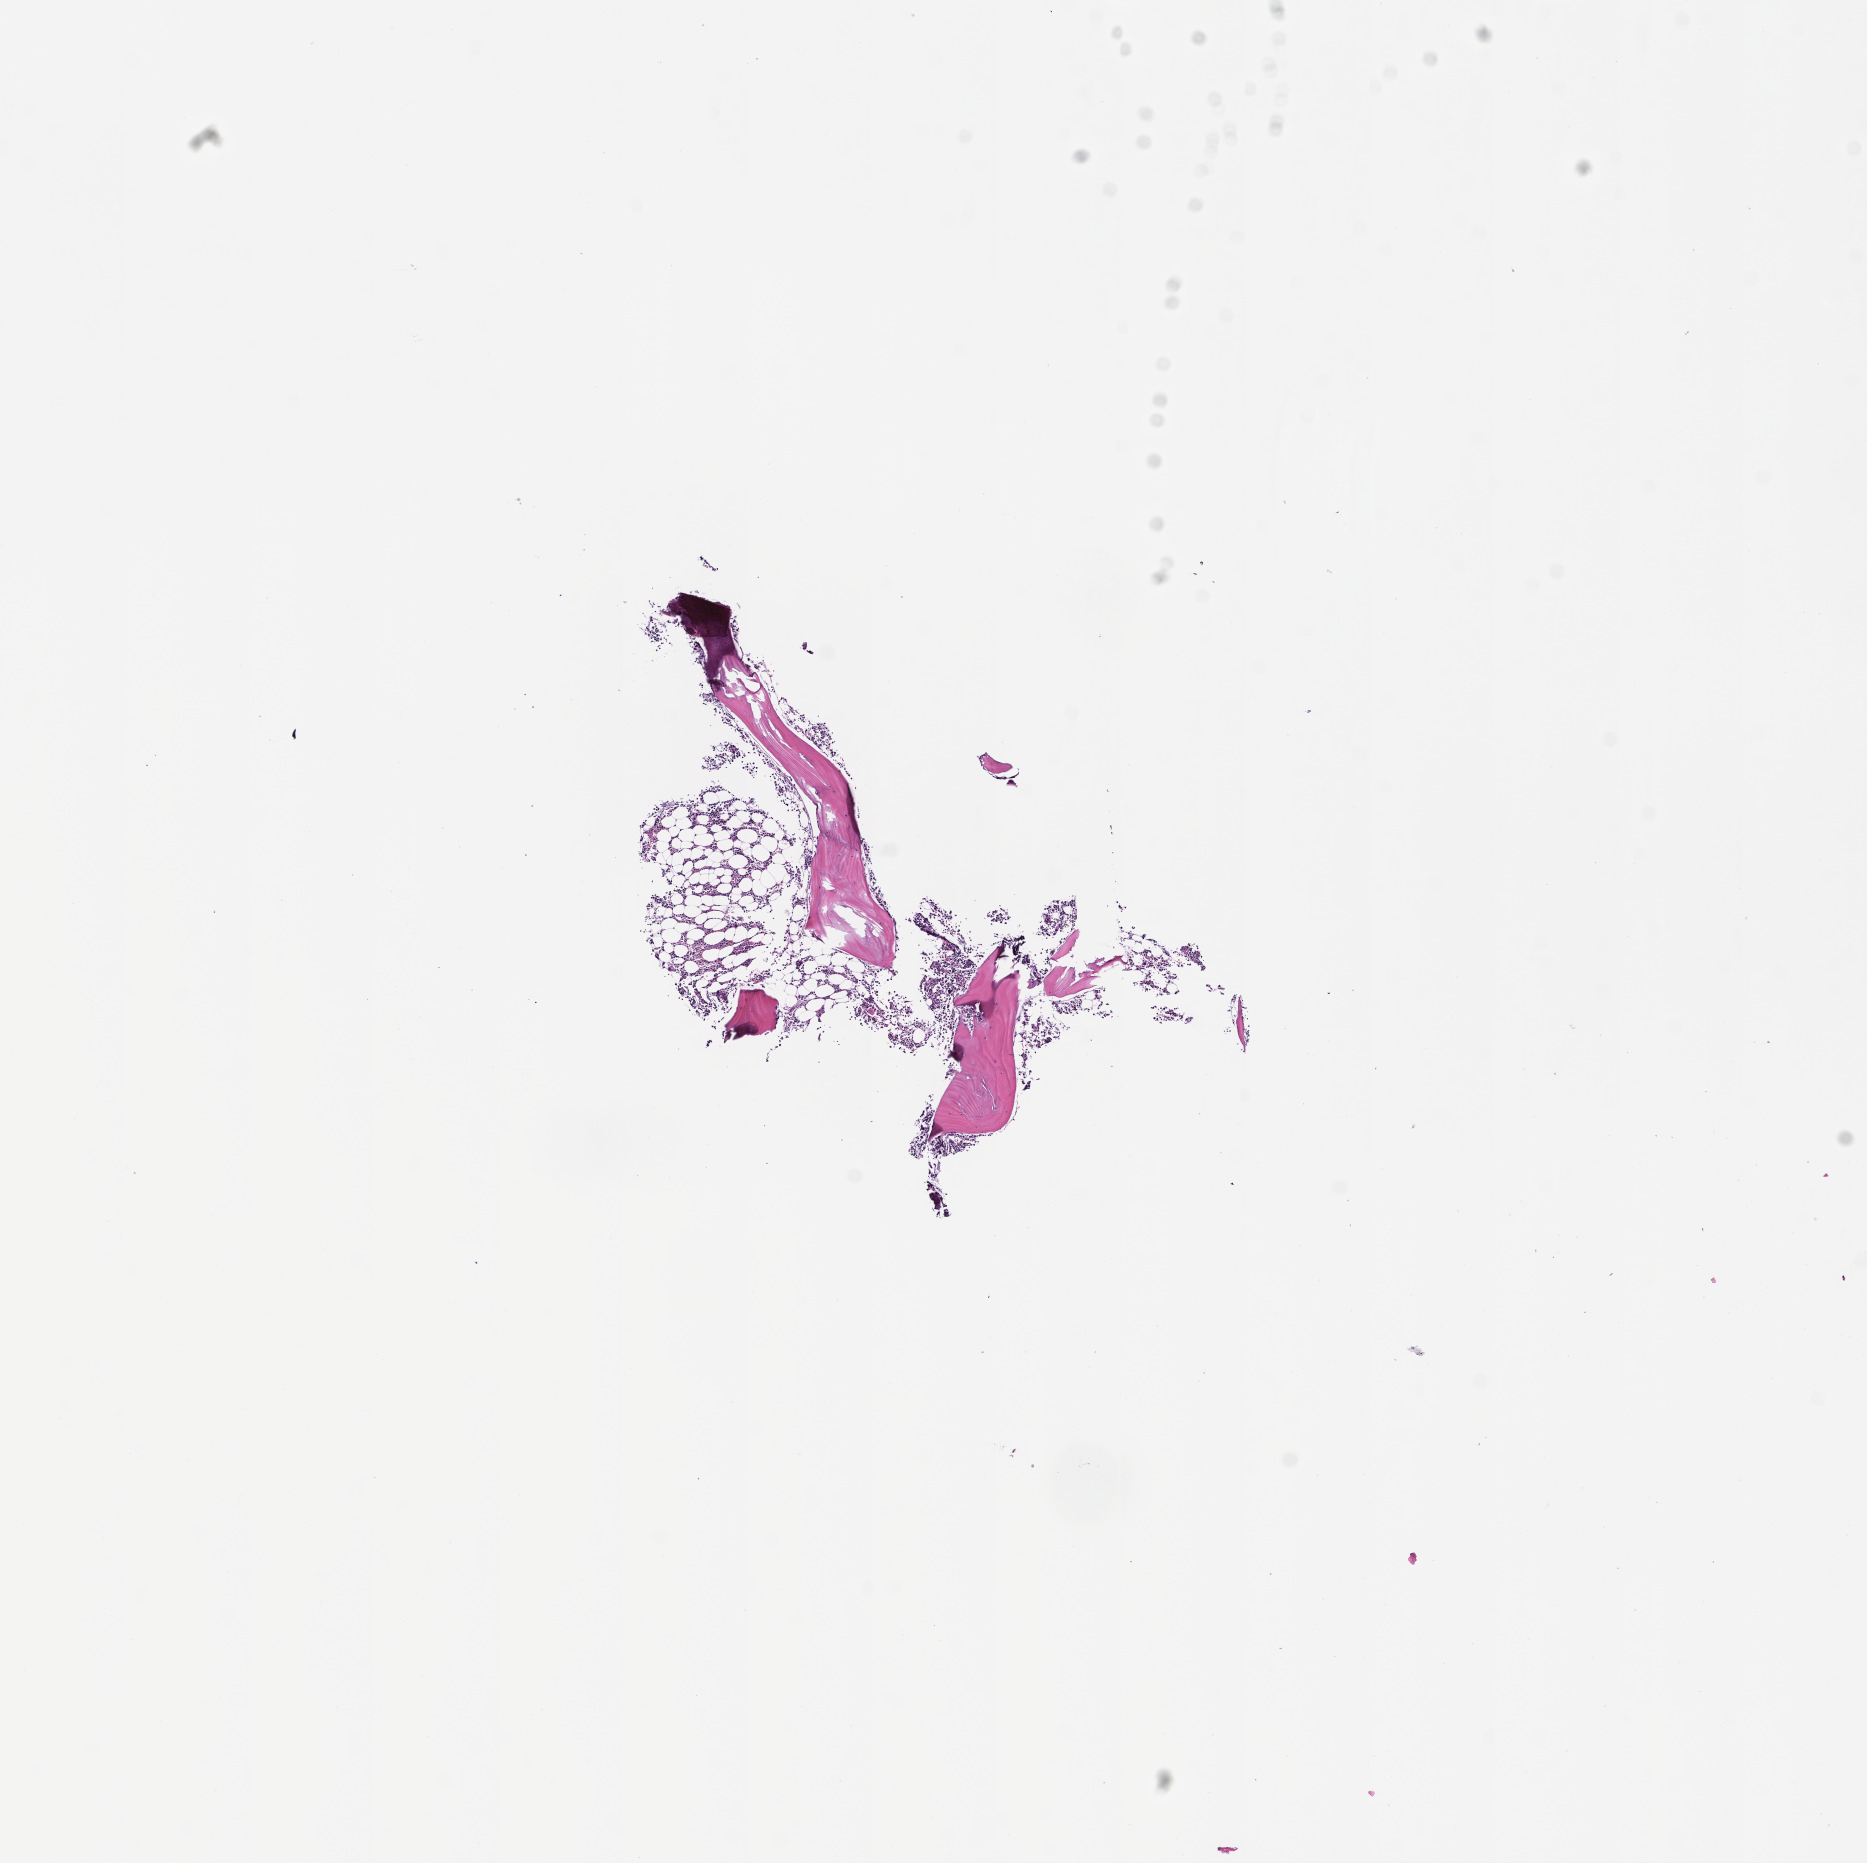
Digitized H&E-stained section, a low-resolution overview of the entire scanned area, about 7.5 x 7.5 mm, formalin-fixed paraffin-embedded section, tissue site: bone marrow. Male patient.
* this section: primary tumor
* diagnosis: Plasma Cell Myeloma